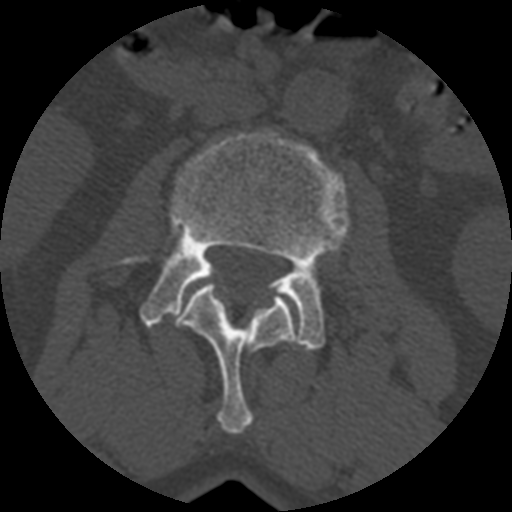
CT including the spine, one axial slice. Reconstruction kernel STANDARD. Bone window (W 1800 / L 400 HU). 512 × 512 image matrix, field of view 160 × 160 mm. Patient age 71 years. Case-level facts recorded for this patient, not image findings: primary cancer: prostate.
Outlined on this slice (semi-automatically segmented with operator editing):
- L2 vertebra: box from (x=174, y=283) to (x=295, y=435) px
- L3 vertebra: (x=116, y=130)–(x=348, y=350)